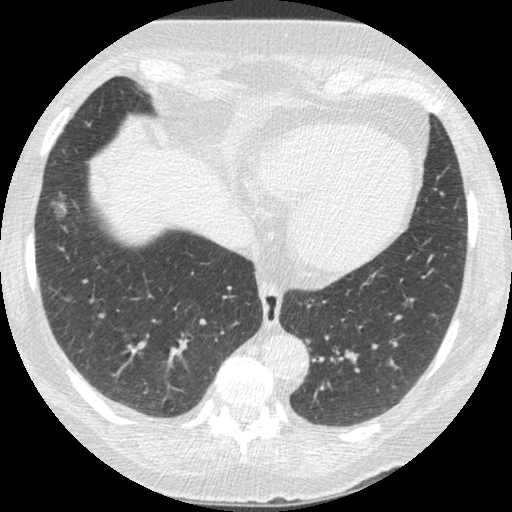
Low-dose screening chest CT, one axial slice. Slice 87 of 245 in the series (ordered by position). Reconstruction kernel STANDARD. 120 kVp. Lung window (W 1500 / L -600 HU). 1.25 mm slice thickness. 512 × 512 image matrix, field of view 310 × 310 mm.
Structures marked on this image (outlined manually by an expert reader):
- lesion 1 (tumor, lower lobe of right lung): bounding box <53,200,68,217> (left, top, right, bottom; pixels)